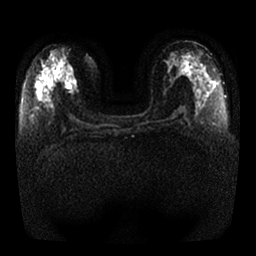
Breast MRI, one axial slice. Position 11 of 25 along the scan axis. Diffusion-weighted series; image 2 of 4 stored at this slice position (different b-values; order by instance number). 1.5 T. 4 mm slice thickness. 256 × 256 image matrix, field of view 350 × 350 mm. Female patient.
Outlined on this slice (expert manual segmentation):
- tumour on diffusion-weighted imaging: box from (x=65, y=77) to (x=76, y=90) px